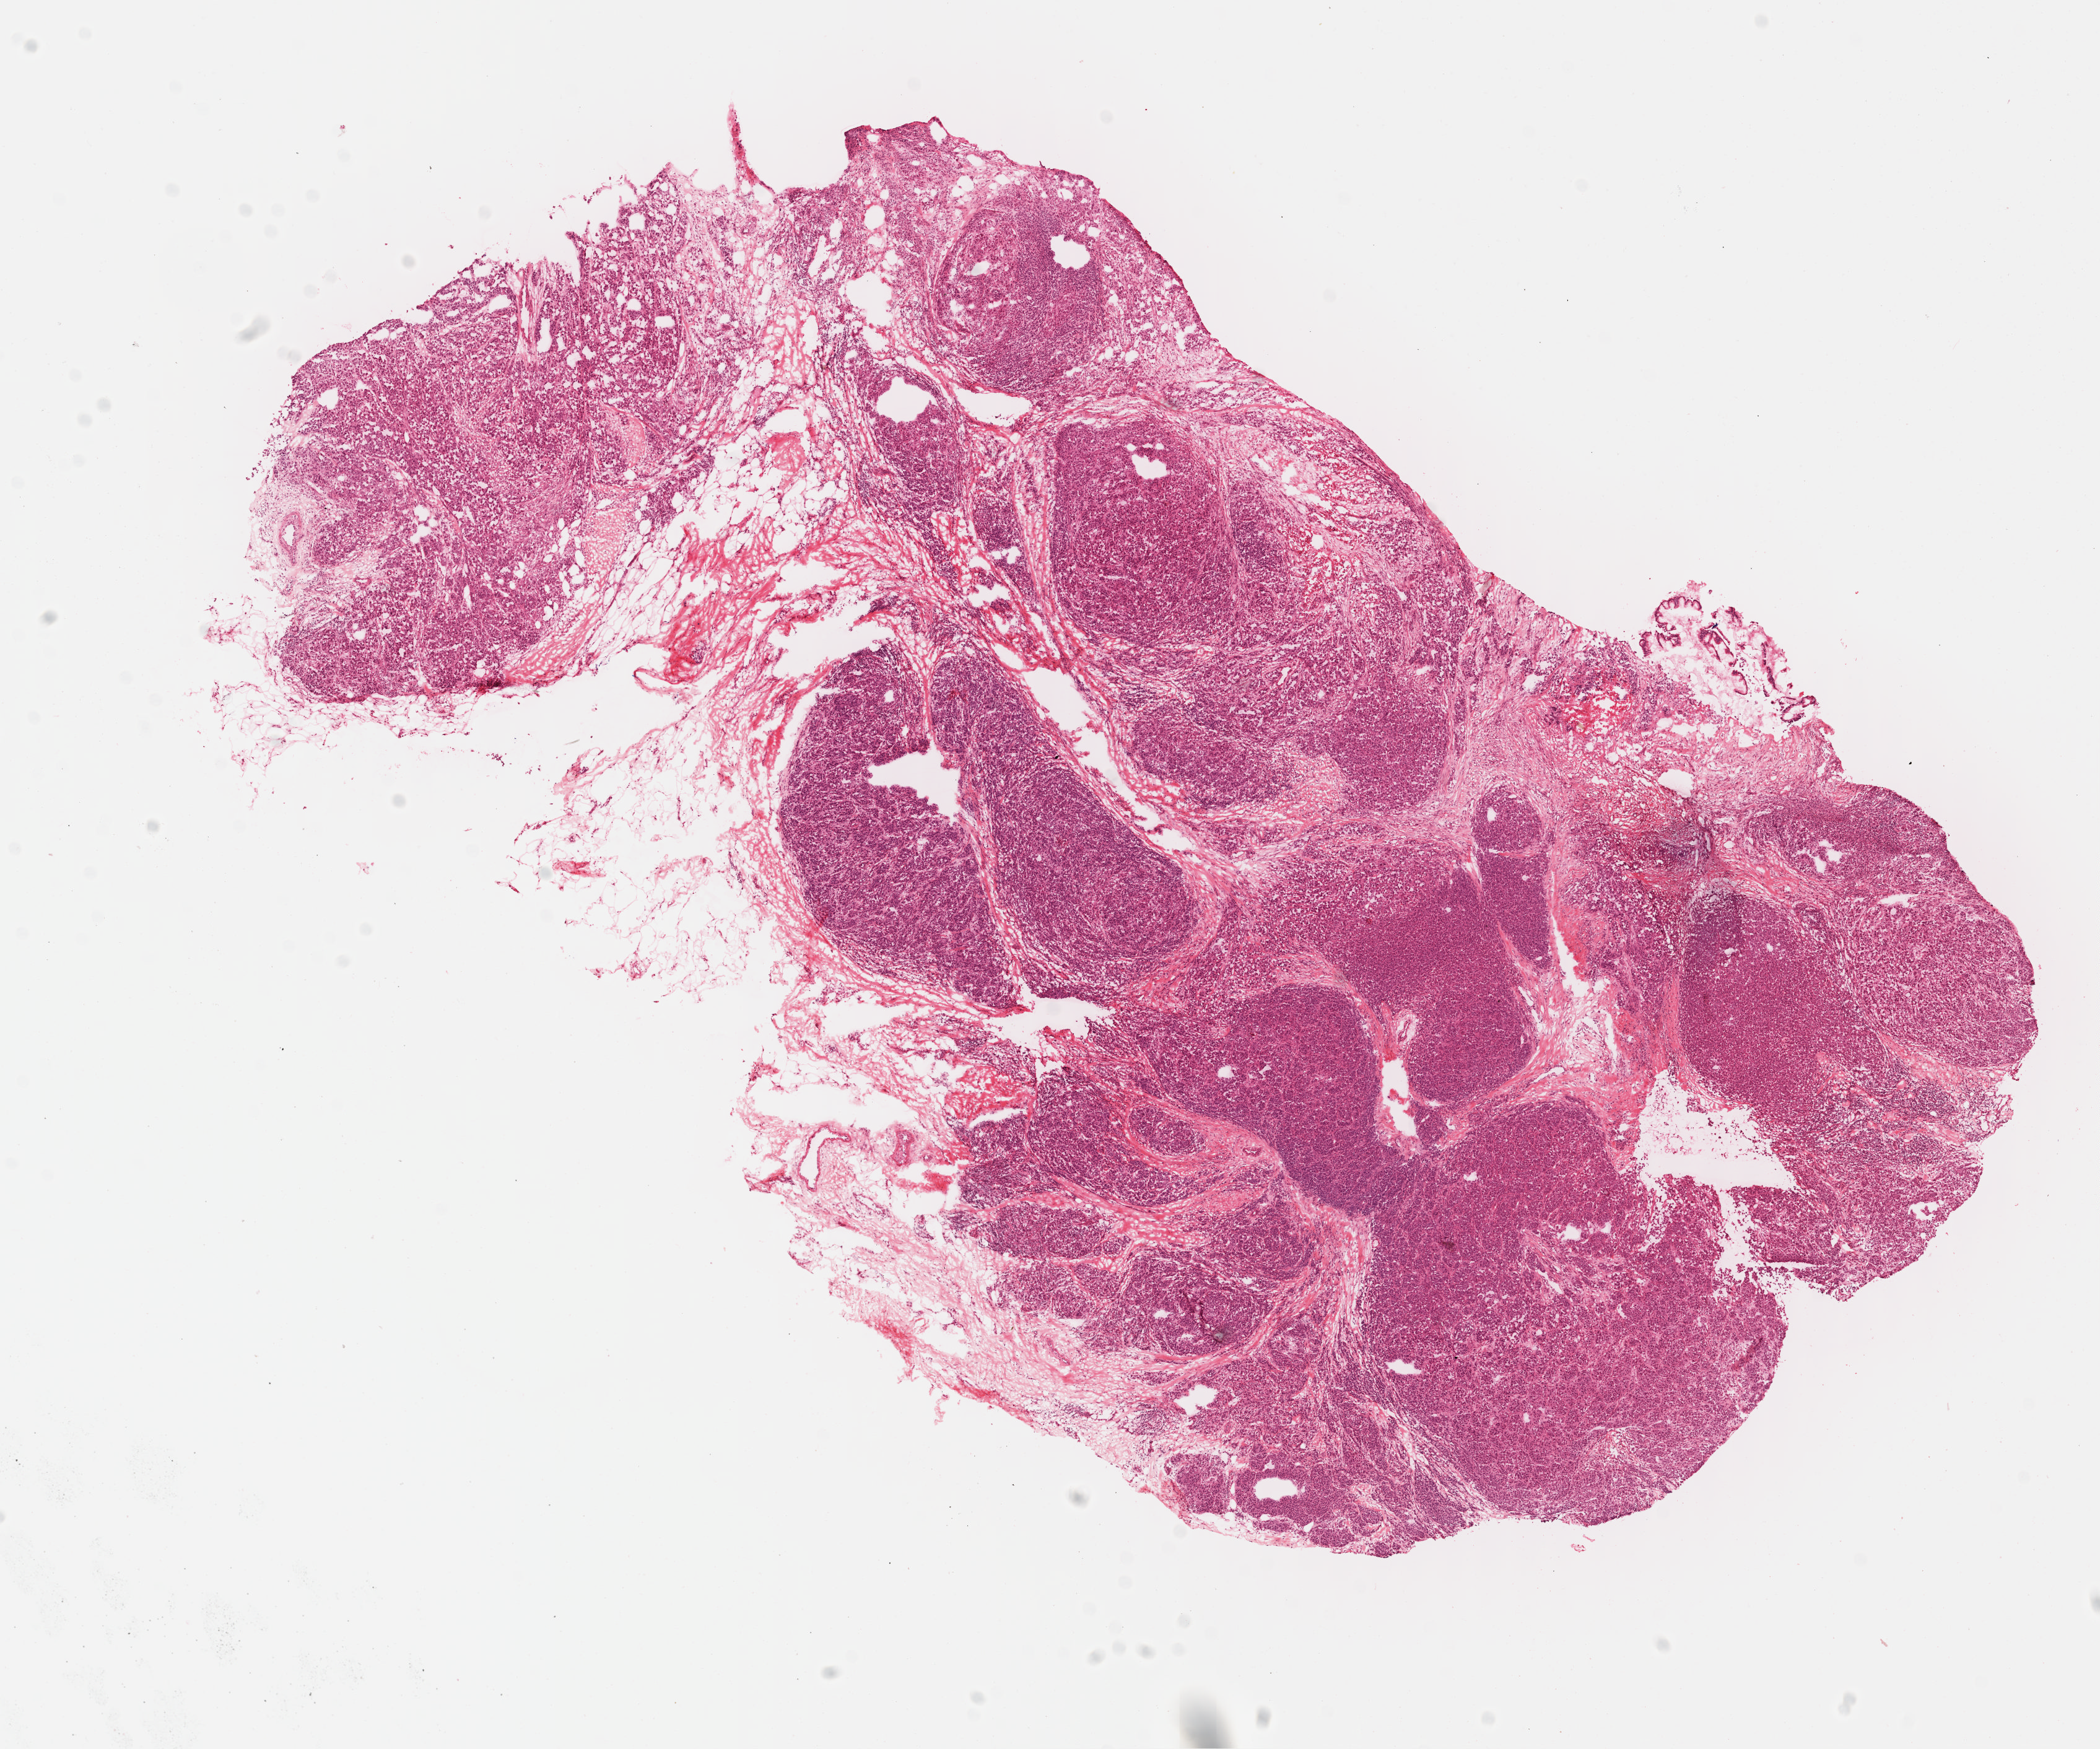
Digitized H&E tissue section (whole slide), shown as a low-resolution overview of the whole scanned area (about 13.3 x 11.1 mm, slide scanned at 40x). FFPE section. Primary tumour sample from the skin. Patient: male, age at initial diagnosis 42 years.
* histologic diagnosis: Amelanotic melanoma